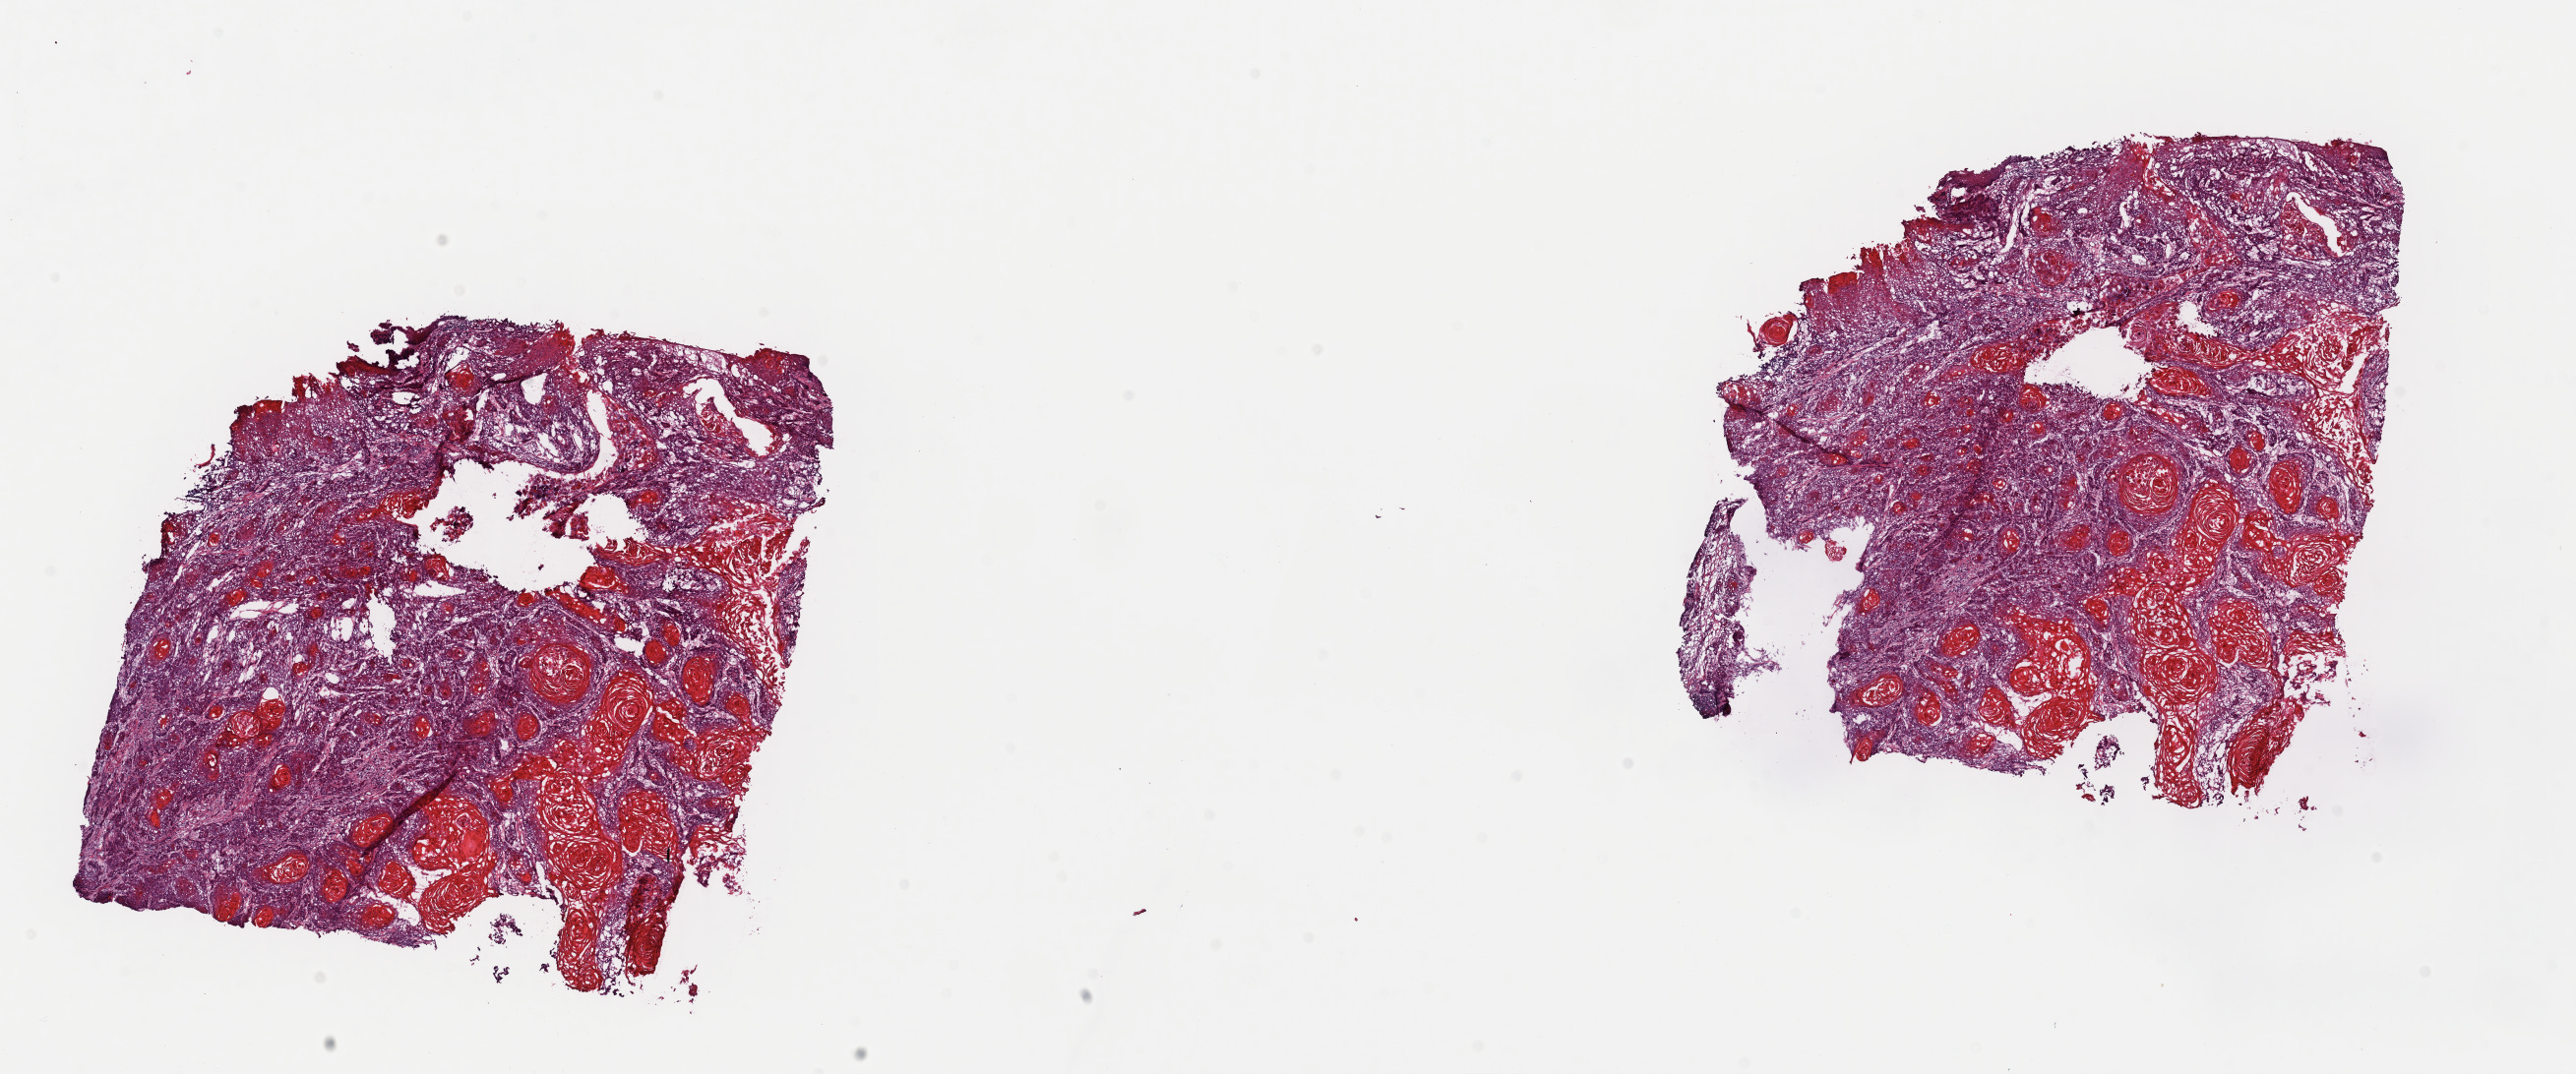
Digitized H&E tissue section (whole slide) — low-resolution overview of the scanned area, about 20.7 x 8.6 mm (slide scanned at 40x). Frozen section from the top of the tissue portion. Sample: primary tumour, head and neck. Patient: male, age at initial diagnosis 30 years. Pathologist review of this section (percent, as recorded): tumour cells 90%, tumour nuclei 95%.
Diagnosis: Squamous cell carcinoma, keratinizing, NOS (tongue, NOS).